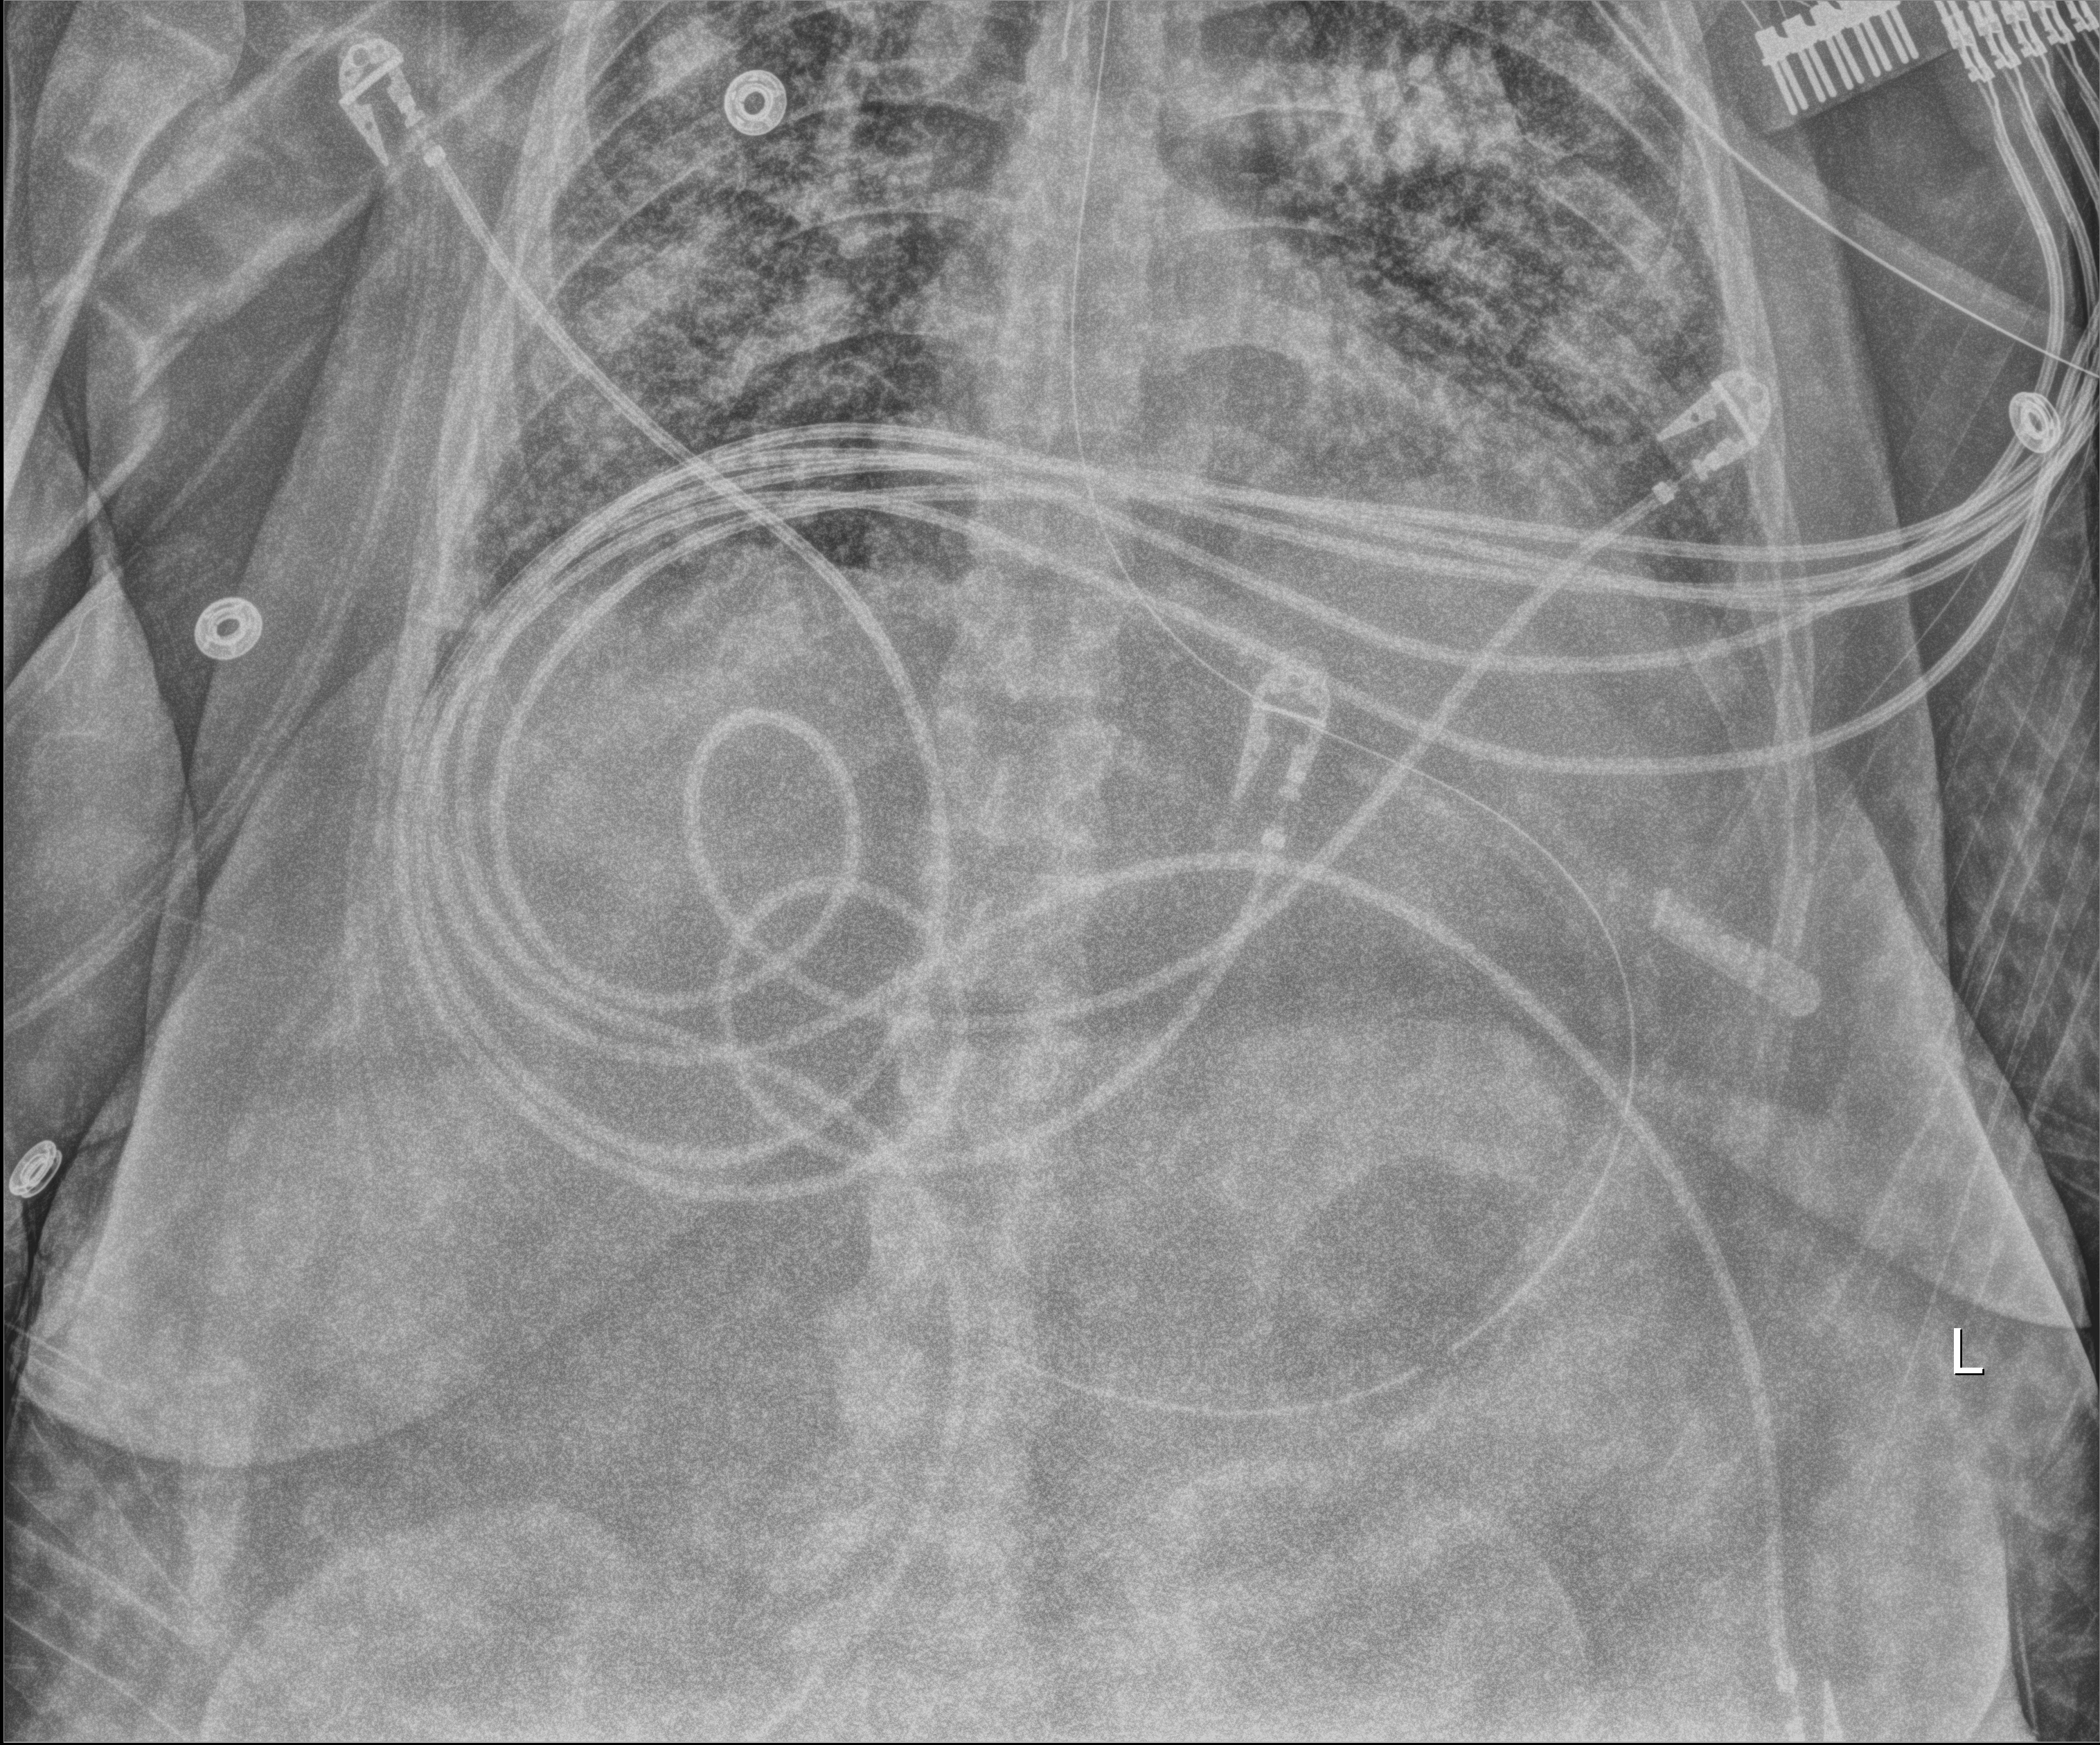
Portable chest radiograph, anteroposterior (AP) projection. Female patient hospitalised with COVID-19, age 18–59 years.
From the hospital-stay record, not from the radiograph (when in the stay this image was taken is not recorded): mechanically ventilated during this hospital stay: yes; length of hospital stay: 33 days; admitted to intensive care during this hospital stay: no.